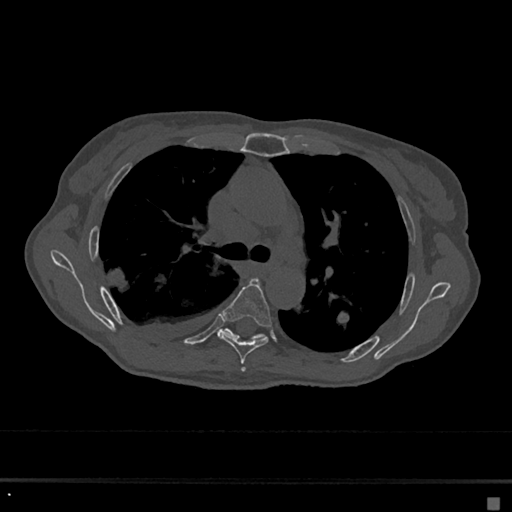
CT including the spine, one axial slice; slice 452 of 797 in the series (ordered by position); bone window (W 1800 / L 400 HU); 512 × 512 image matrix, field of view 360 × 360 mm. Female patient, age 68 years. From the clinical record (not read from this slice): primary cancer: renal.
Annotated regions visible in this slice (semi-automatic segmentation, software-assisted and operator-edited):
- T5 vertebra: bounding box <220,278,272,370> (left, top, right, bottom; pixels)
- T6 vertebra: <217,328,265,340>